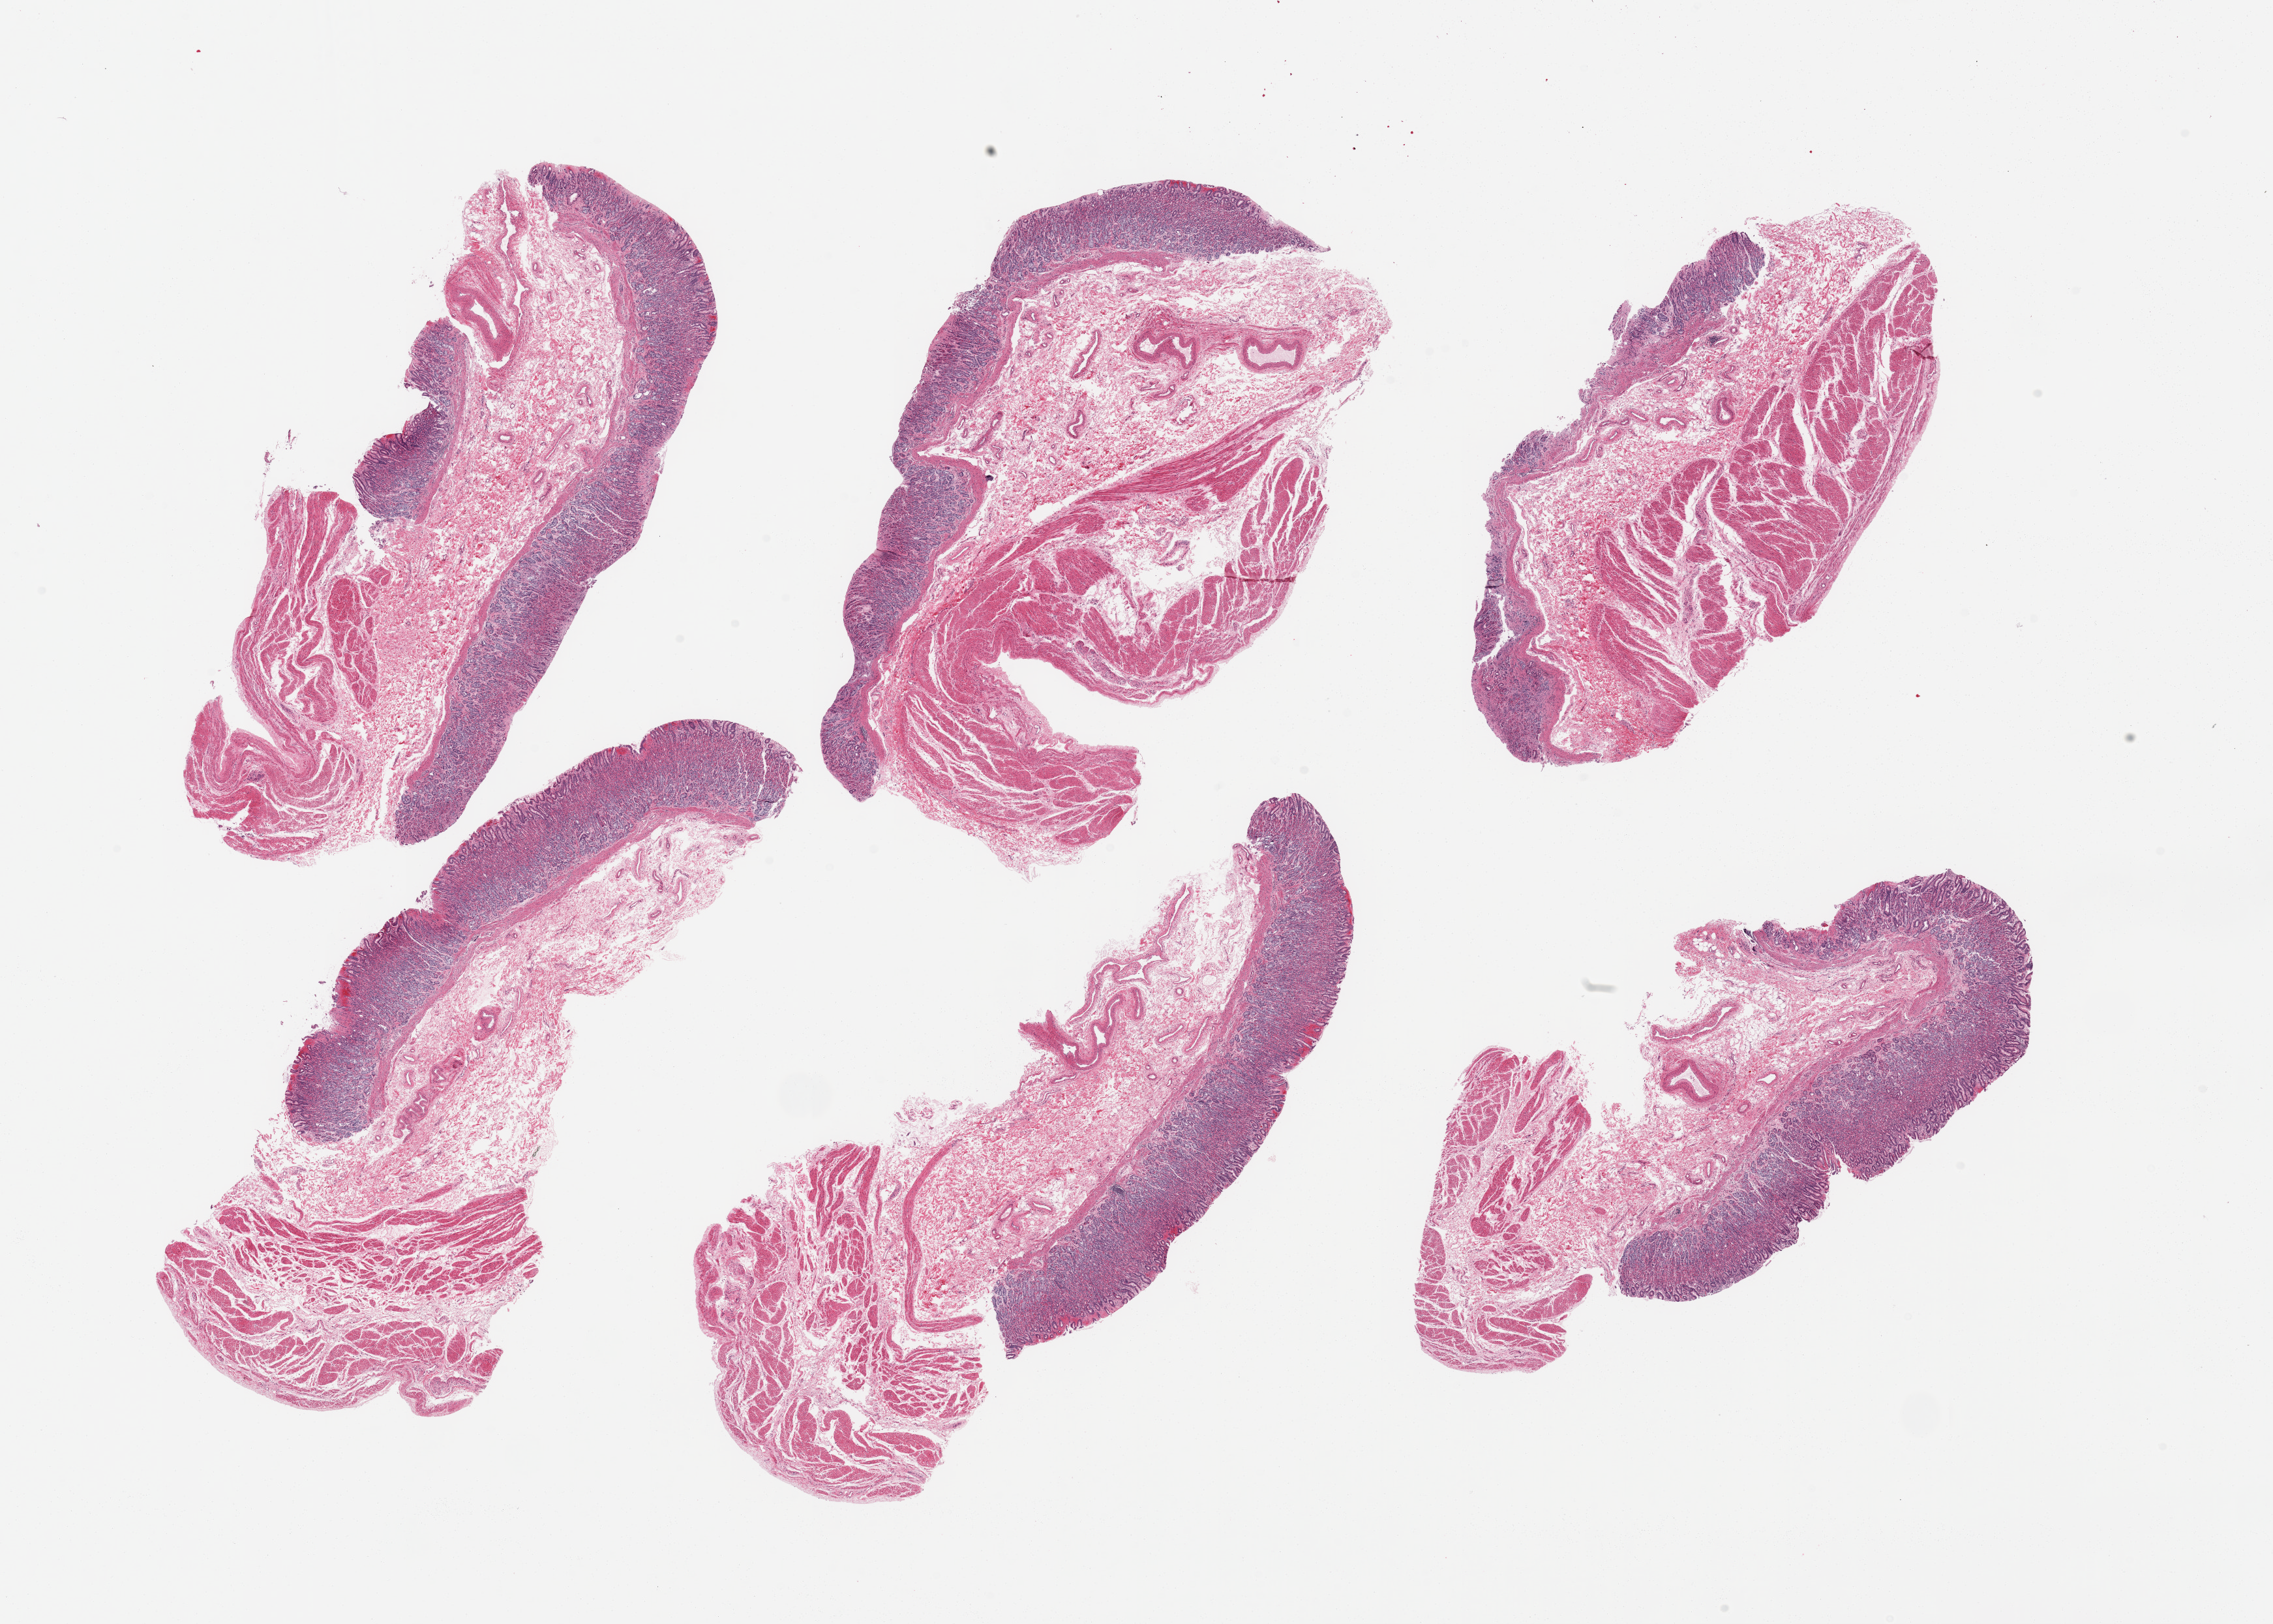
Whole-slide image, hematoxylin and eosin (H&E) stain, whole scanned area (about 27.6 x 19.7 mm, from a 20x scan) shown as a low-resolution overview; PAXgene-fixed, paraffin-embedded tissue; section of stomach (target tissue); tissue donor sample.
- review note (as recorded): 6 pieces; several focal superficial erosions